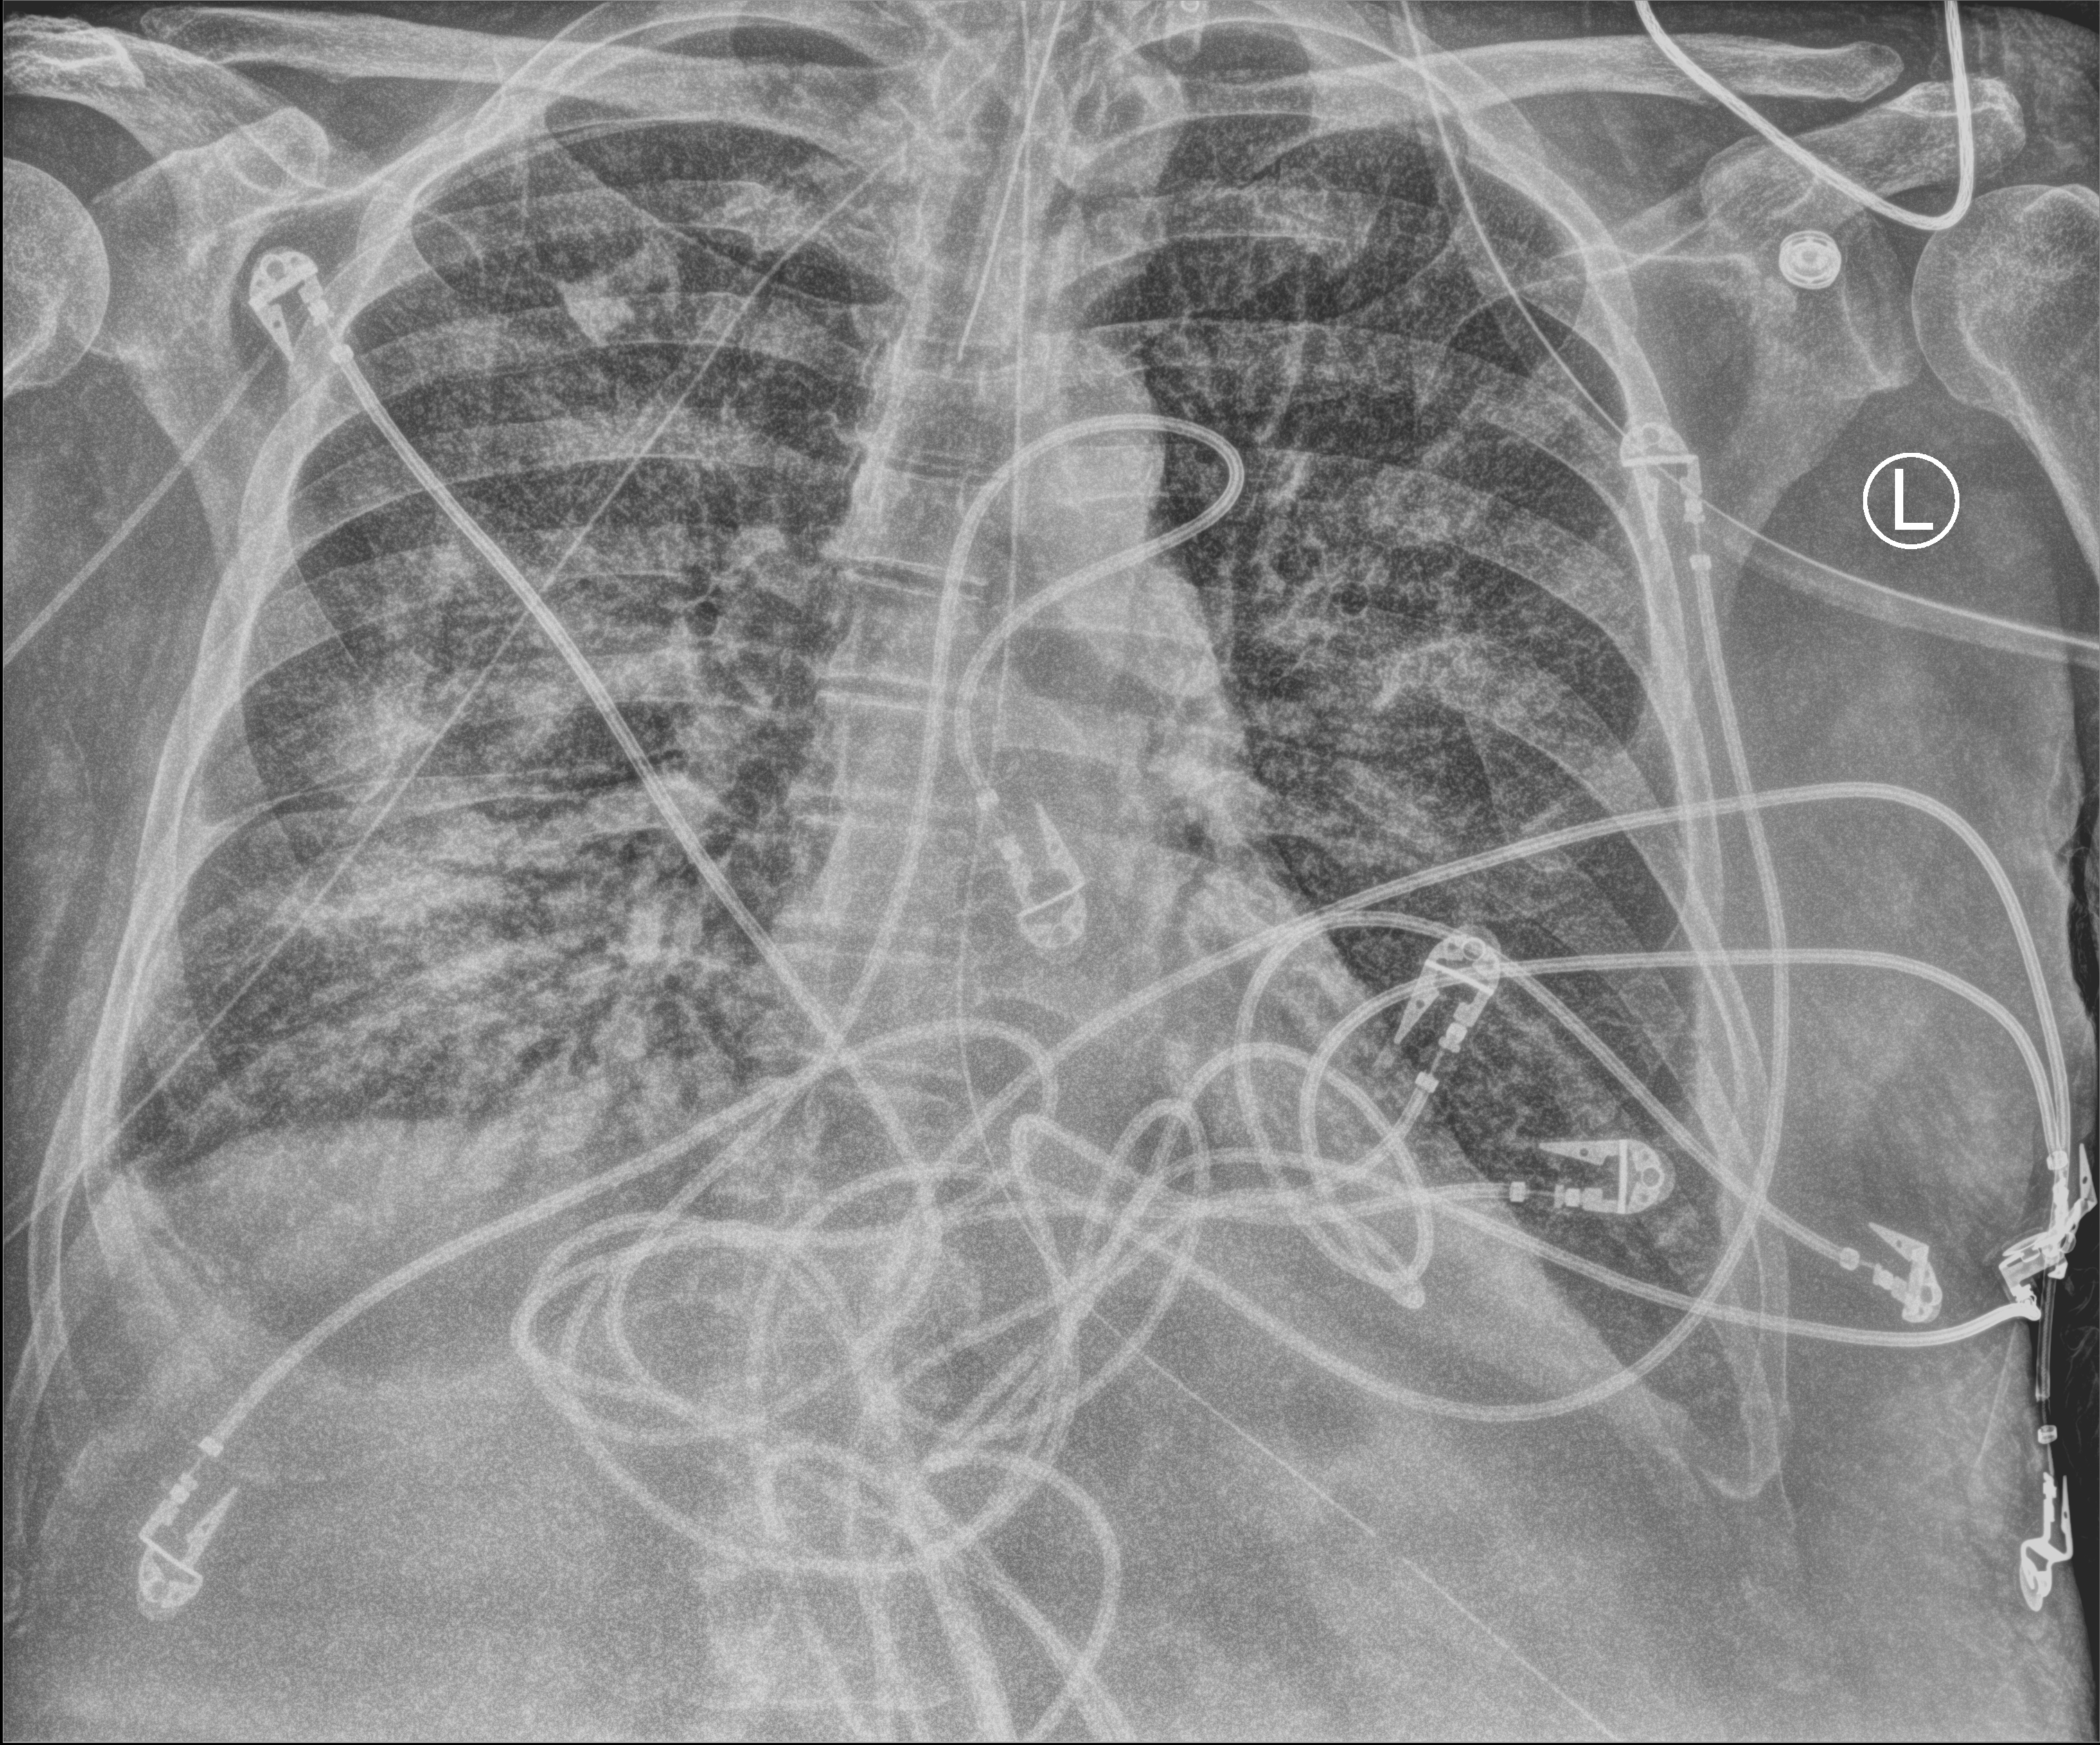
Portable chest radiograph. Patient hospitalised with COVID-19; male, aged 60–74 years.
Hospital-stay facts (about this admission, not read from this image; timing relative to this image not recorded): COPD (admission record): no; smoking status (admission record): former; mechanically ventilated during this hospital stay: yes.